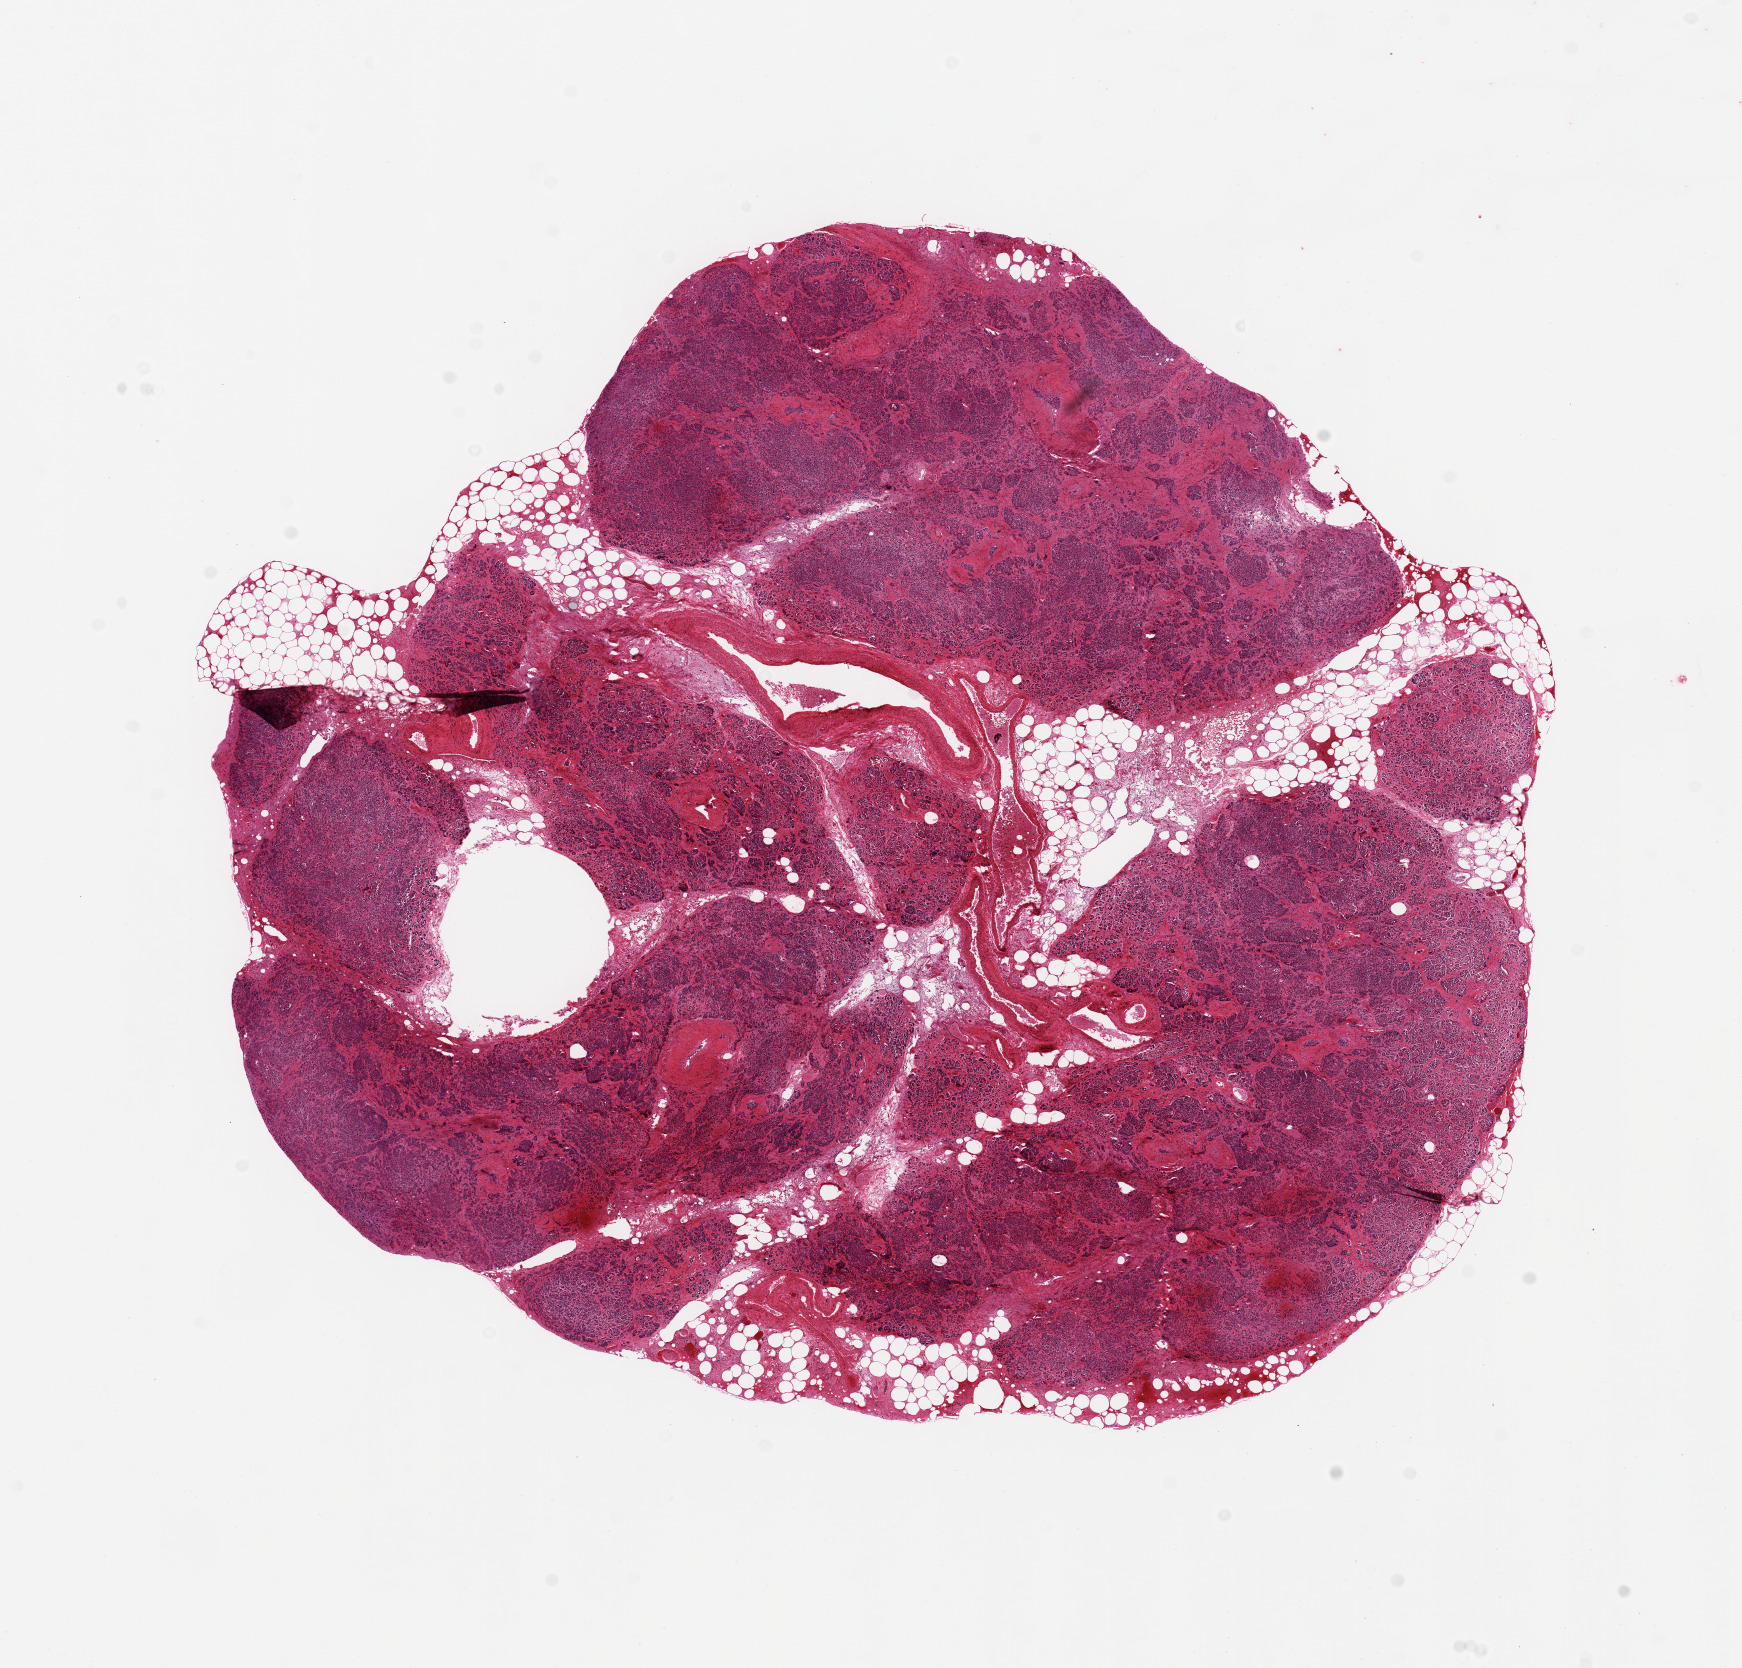
Whole-slide image, H&E stain, whole scanned area (about 13.8 x 13.2 mm, acquisition: 20x scan) shown as a low-resolution overview, PAXgene-fixed paraffin-embedded (PFPE) section, sampled site (target tissue): pancreas, tissue donor sample. Donor: male.
Pathologist's review note for this sample: 10x9 mm; Severe autolysis, but cells intact; 10% fat.